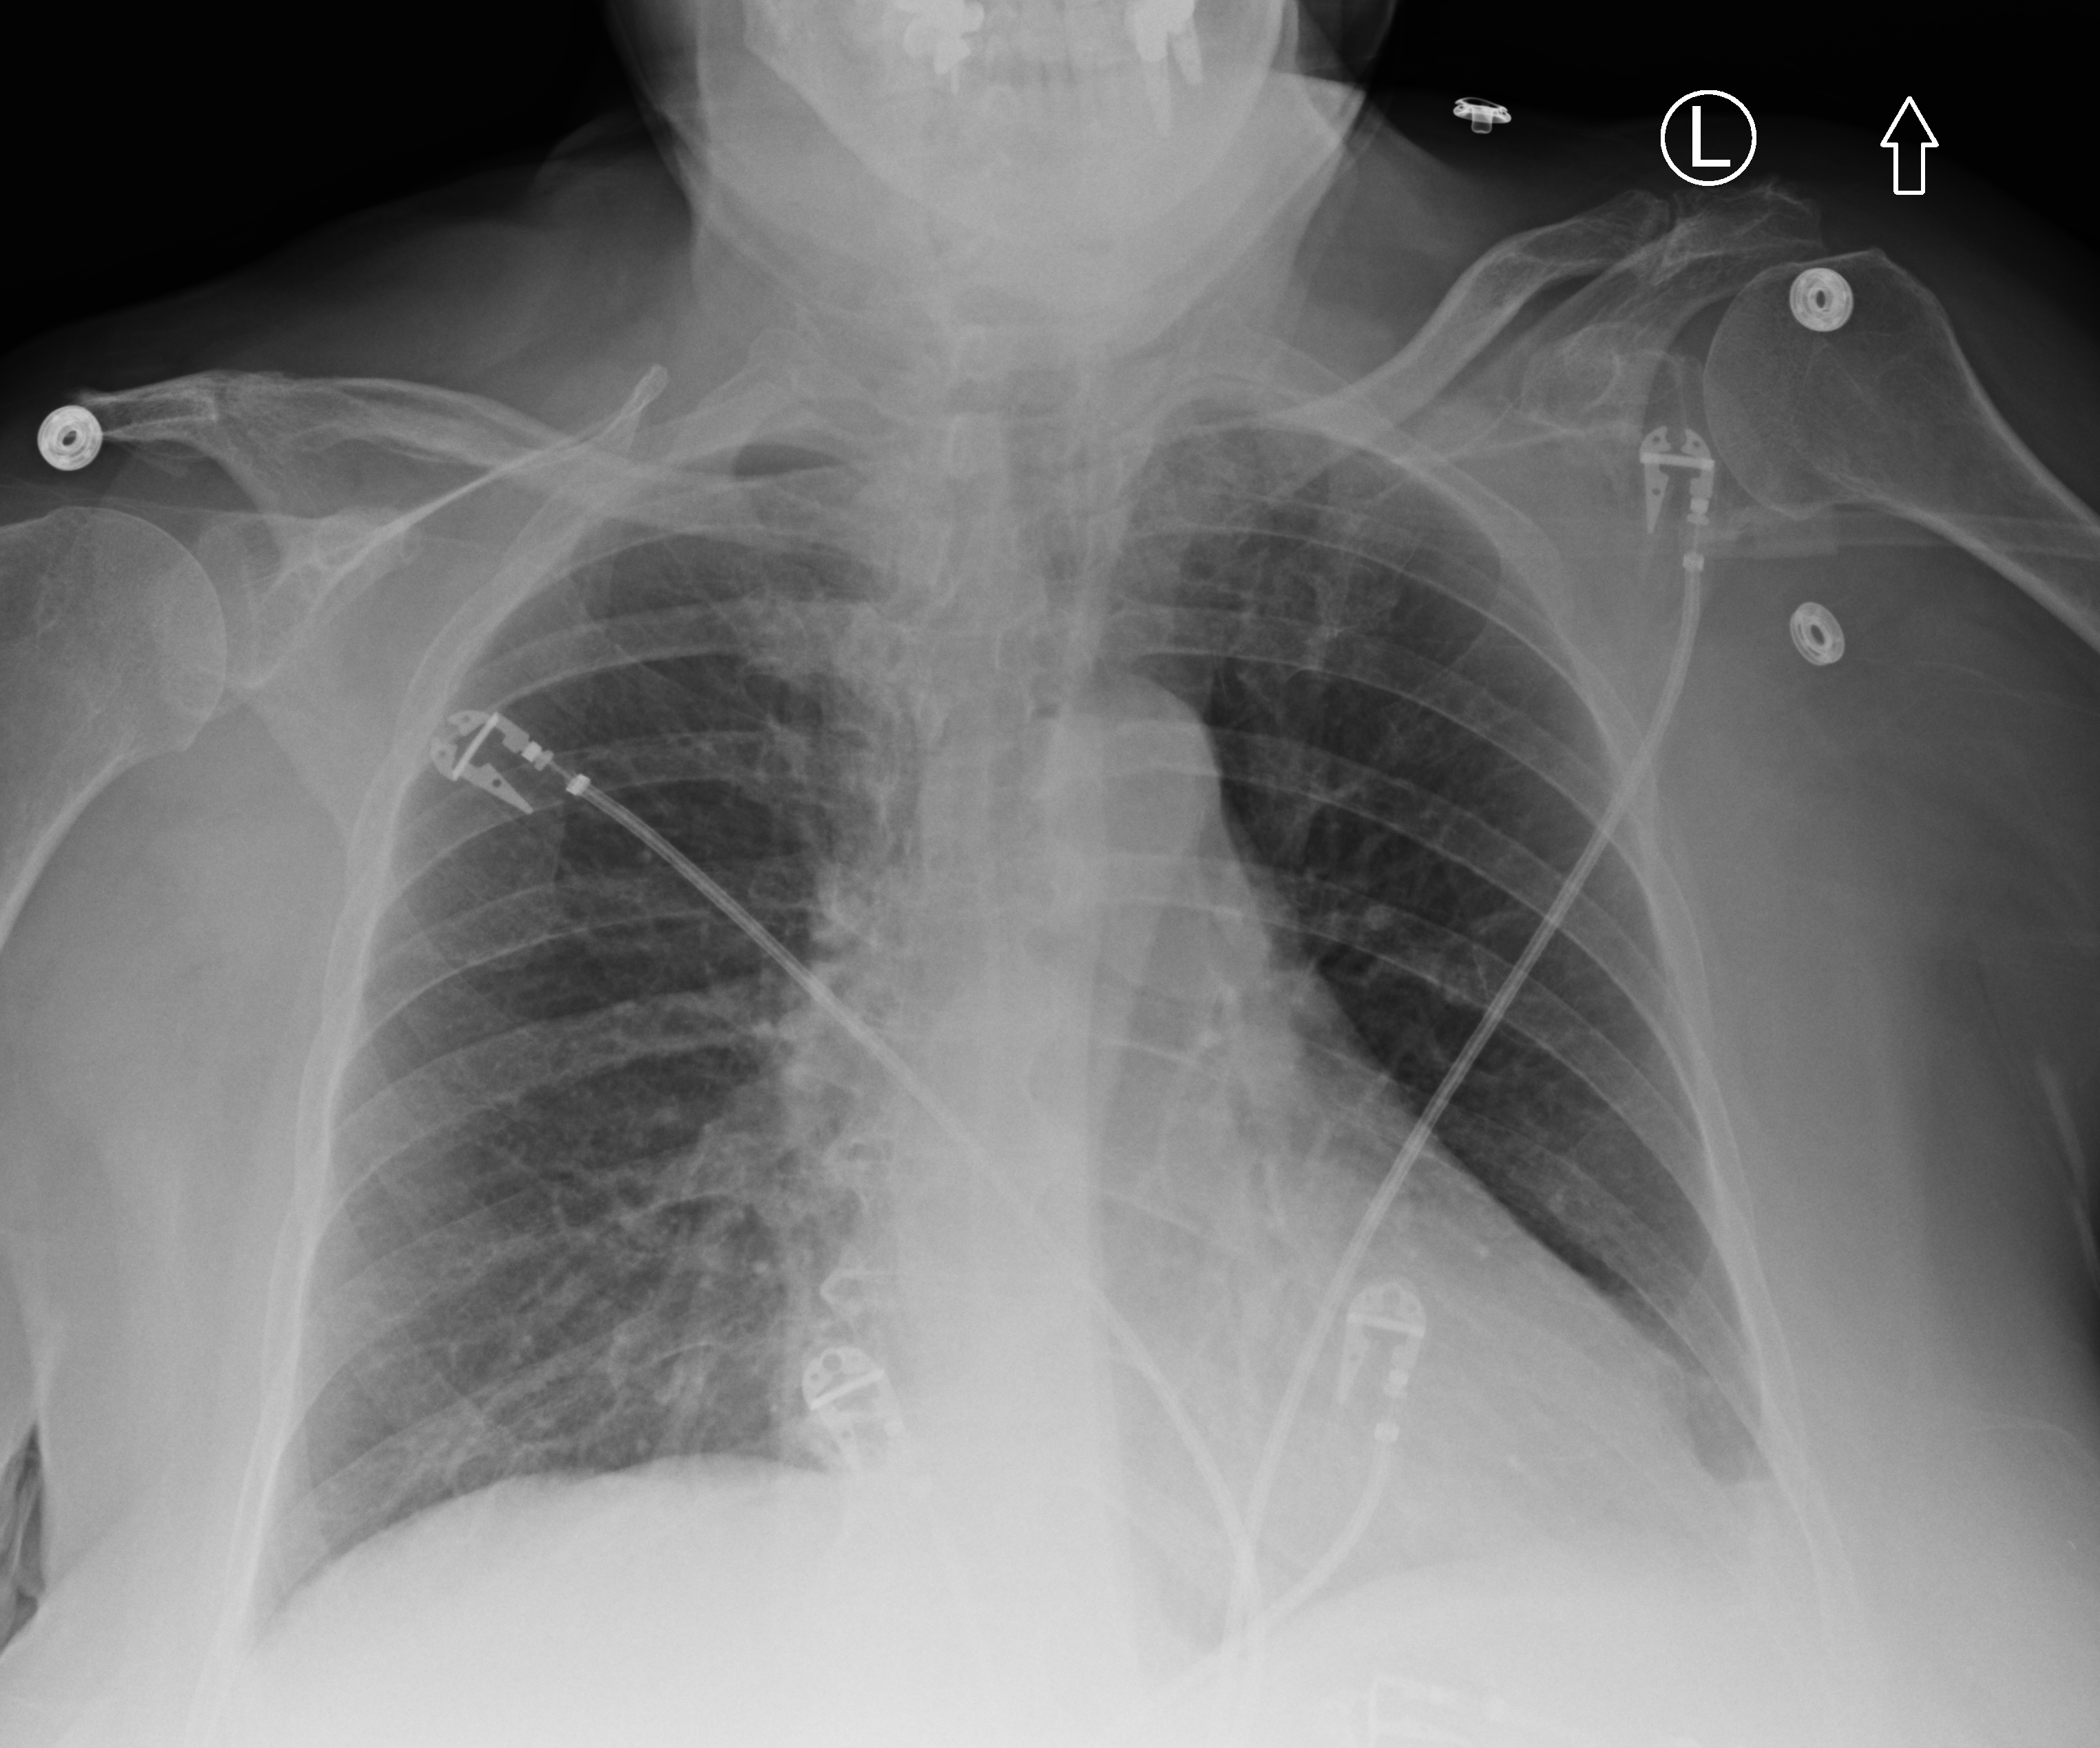
Chest X-ray (portable); anteroposterior (AP) projection. Patient hospitalised with COVID-19; female, aged 60–74 years.
Admission-level facts for this patient (not findings on this image; timing relative to this image not recorded):
- mechanically ventilated during this hospital stay: no
- other chronic lung disease (admission record): no